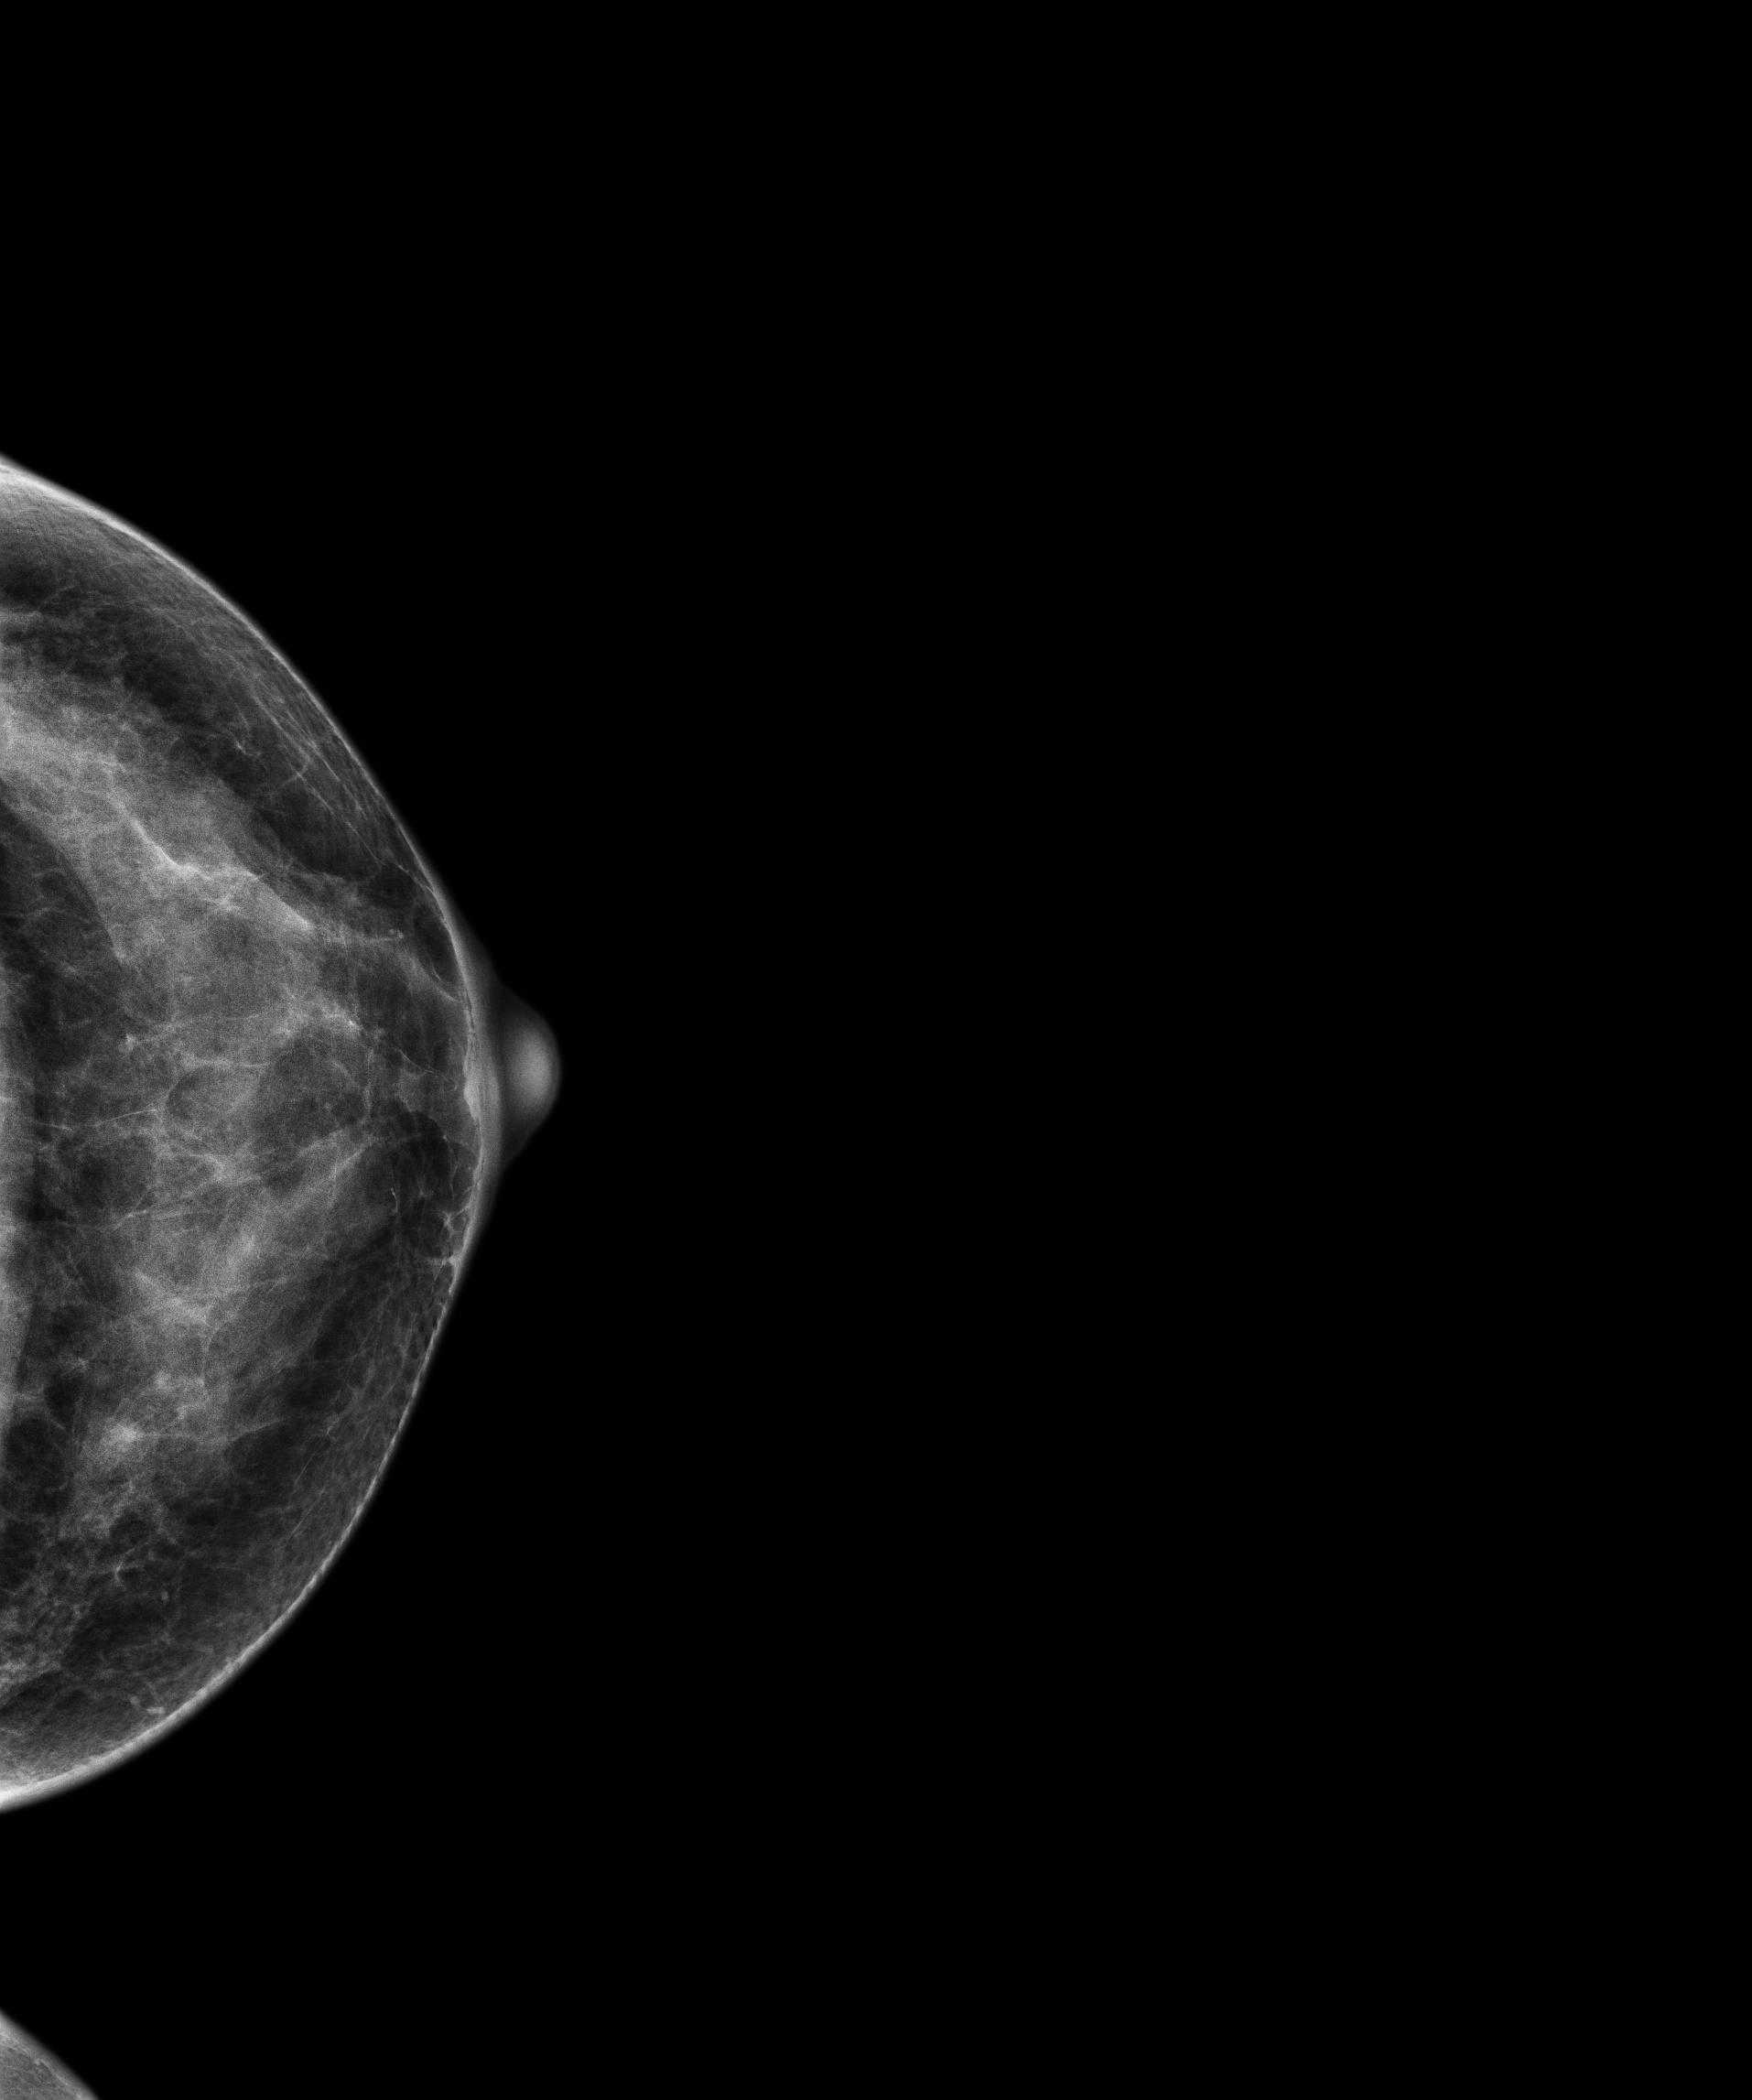
Annual screening mammography examination; compressed breast thickness 38.9 mm. Patient: female, 47 years.
Image type: full-field digital mammogram. Breast: left. Projection: cranio-caudal projection.